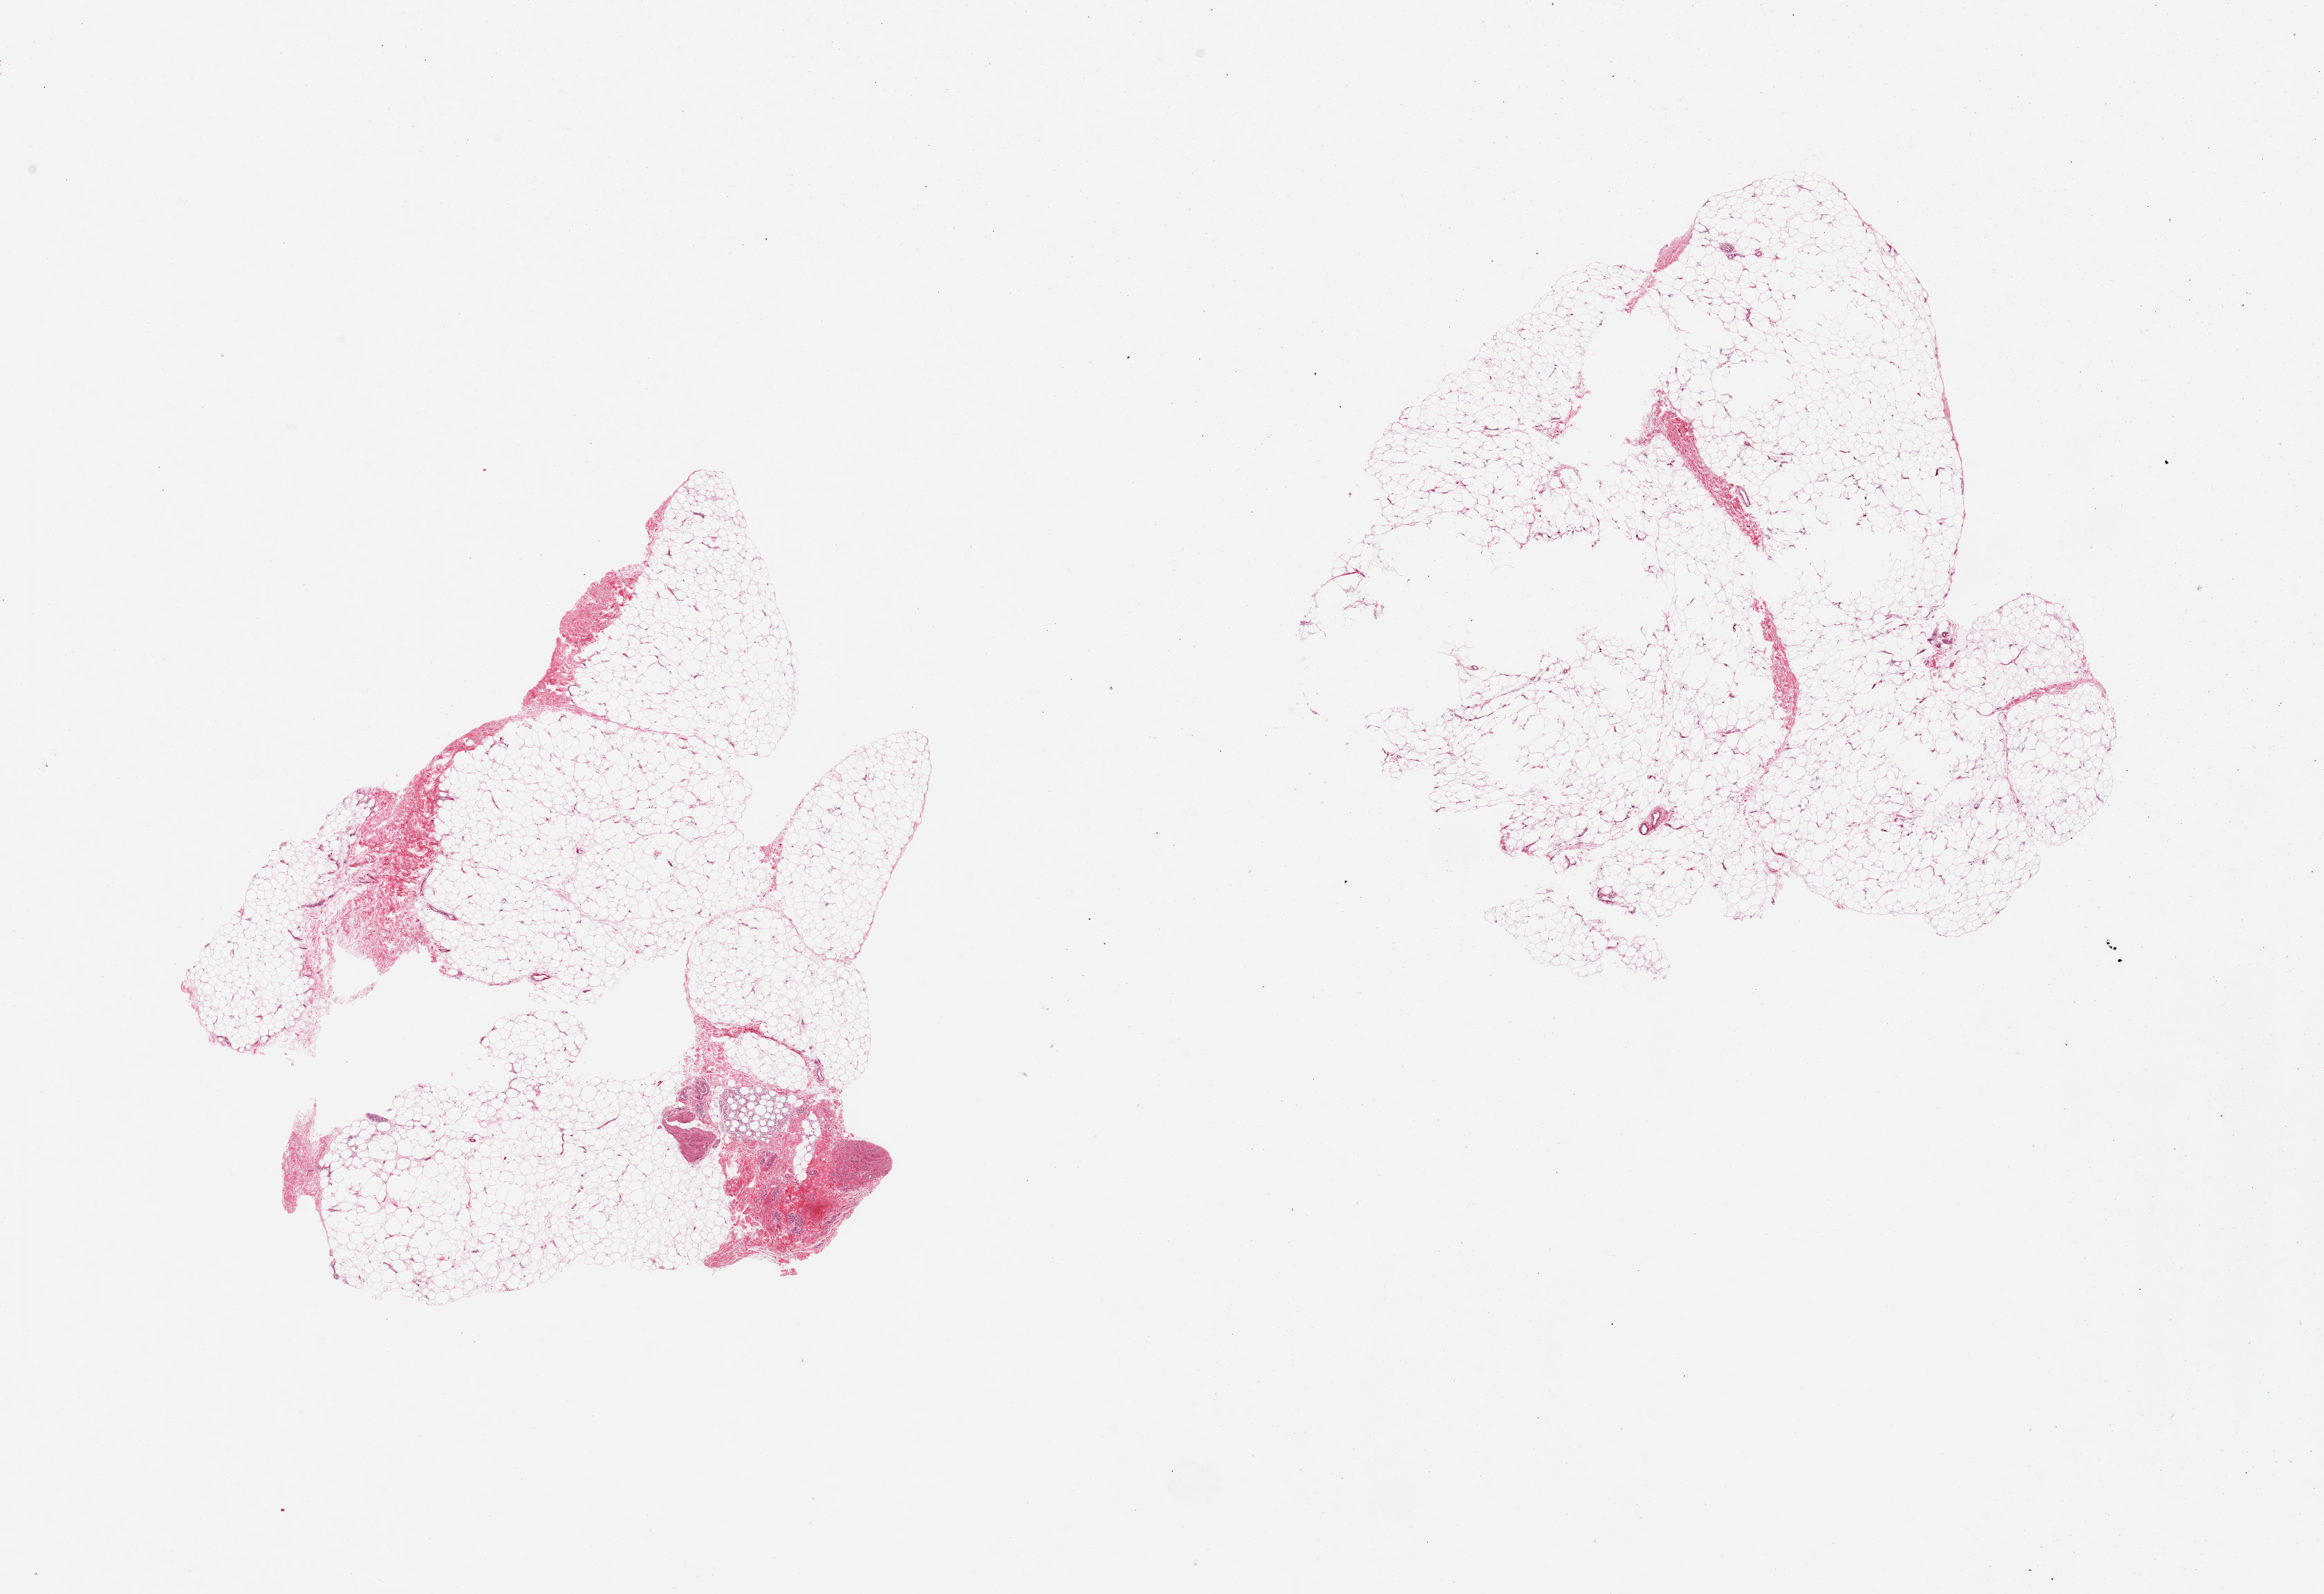
Digitized hematoxylin and eosin (H&E)-stained section, shown as a low-resolution overview of the whole scanned area (about 26.6 x 18.2 mm). PAXgene-fixed paraffin-embedded (PFPE) section. Section of adipose tissue (target tissue). Tissue donor sample.
Review note (as recorded): 2 pieces ~10% fibrous tissue.